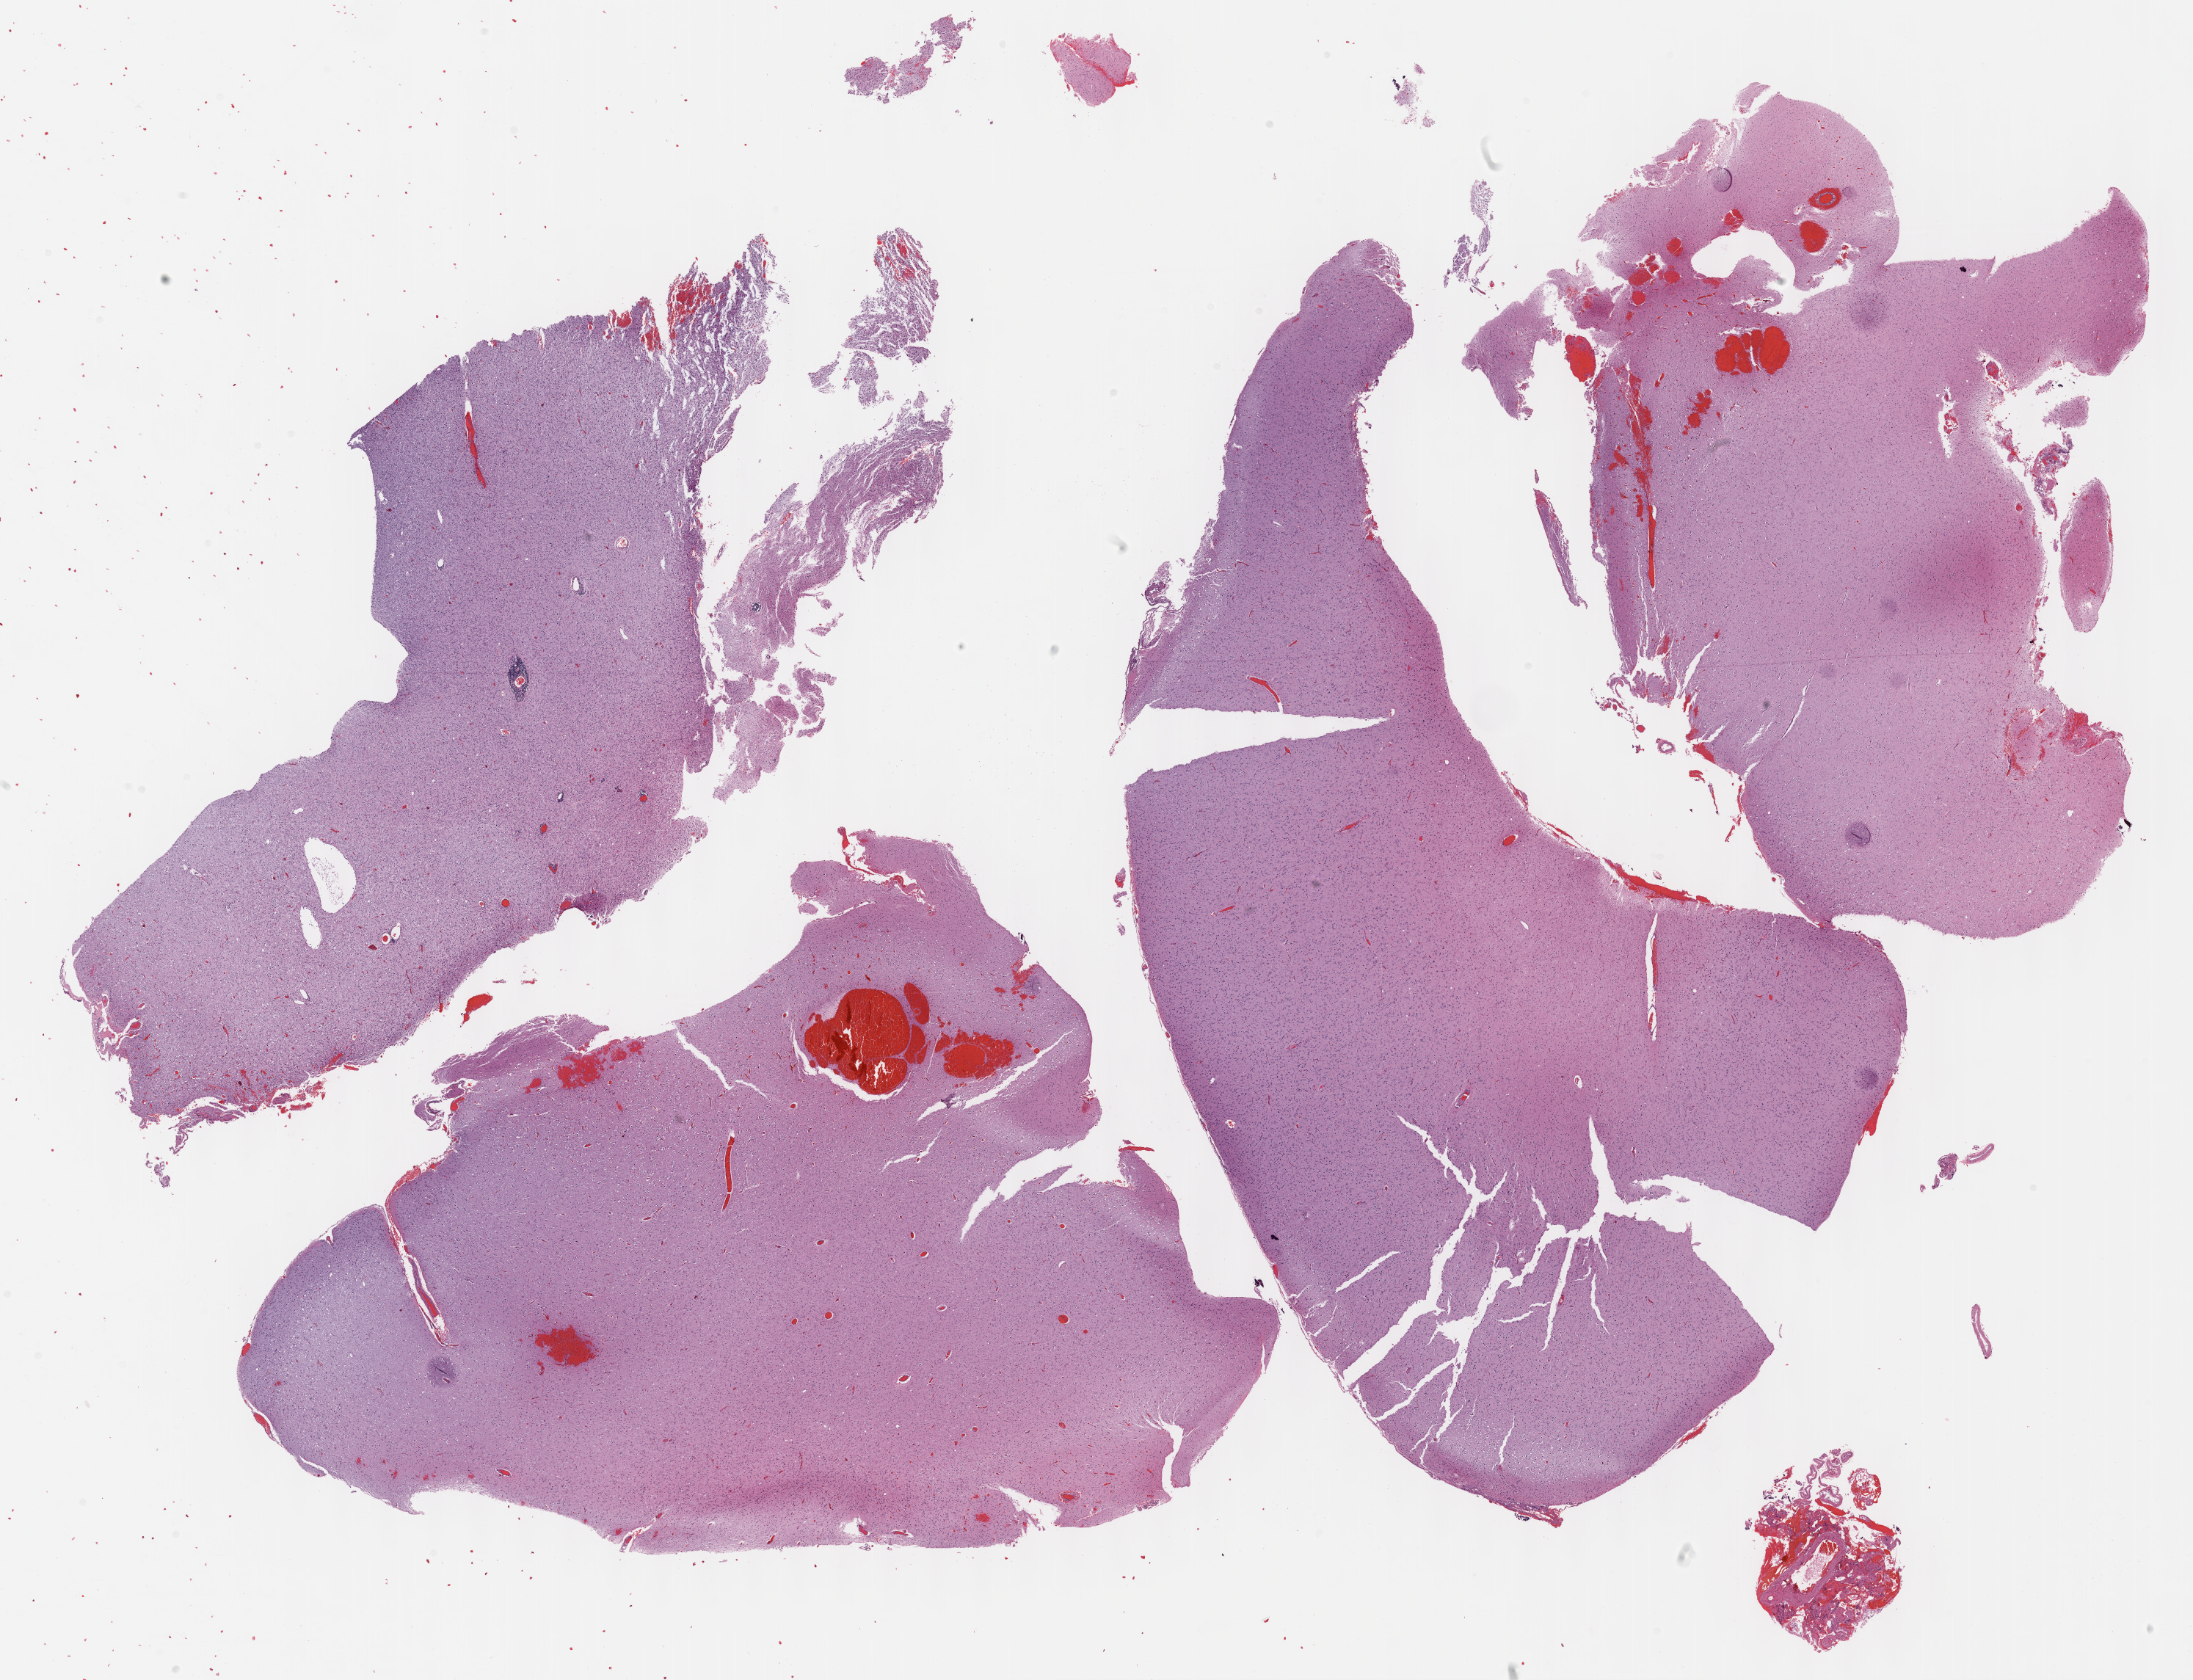
H&E whole-slide image — a low-resolution overview of the entire scanned area, about 24.1 x 18.5 mm, FFPE section, brain, primary tumour sample. Female, age 33 years at initial diagnosis. Histologic grade: G2 (moderately differentiated).
Histologic diagnosis: Oligodendroglioma, NOS (cerebrum).